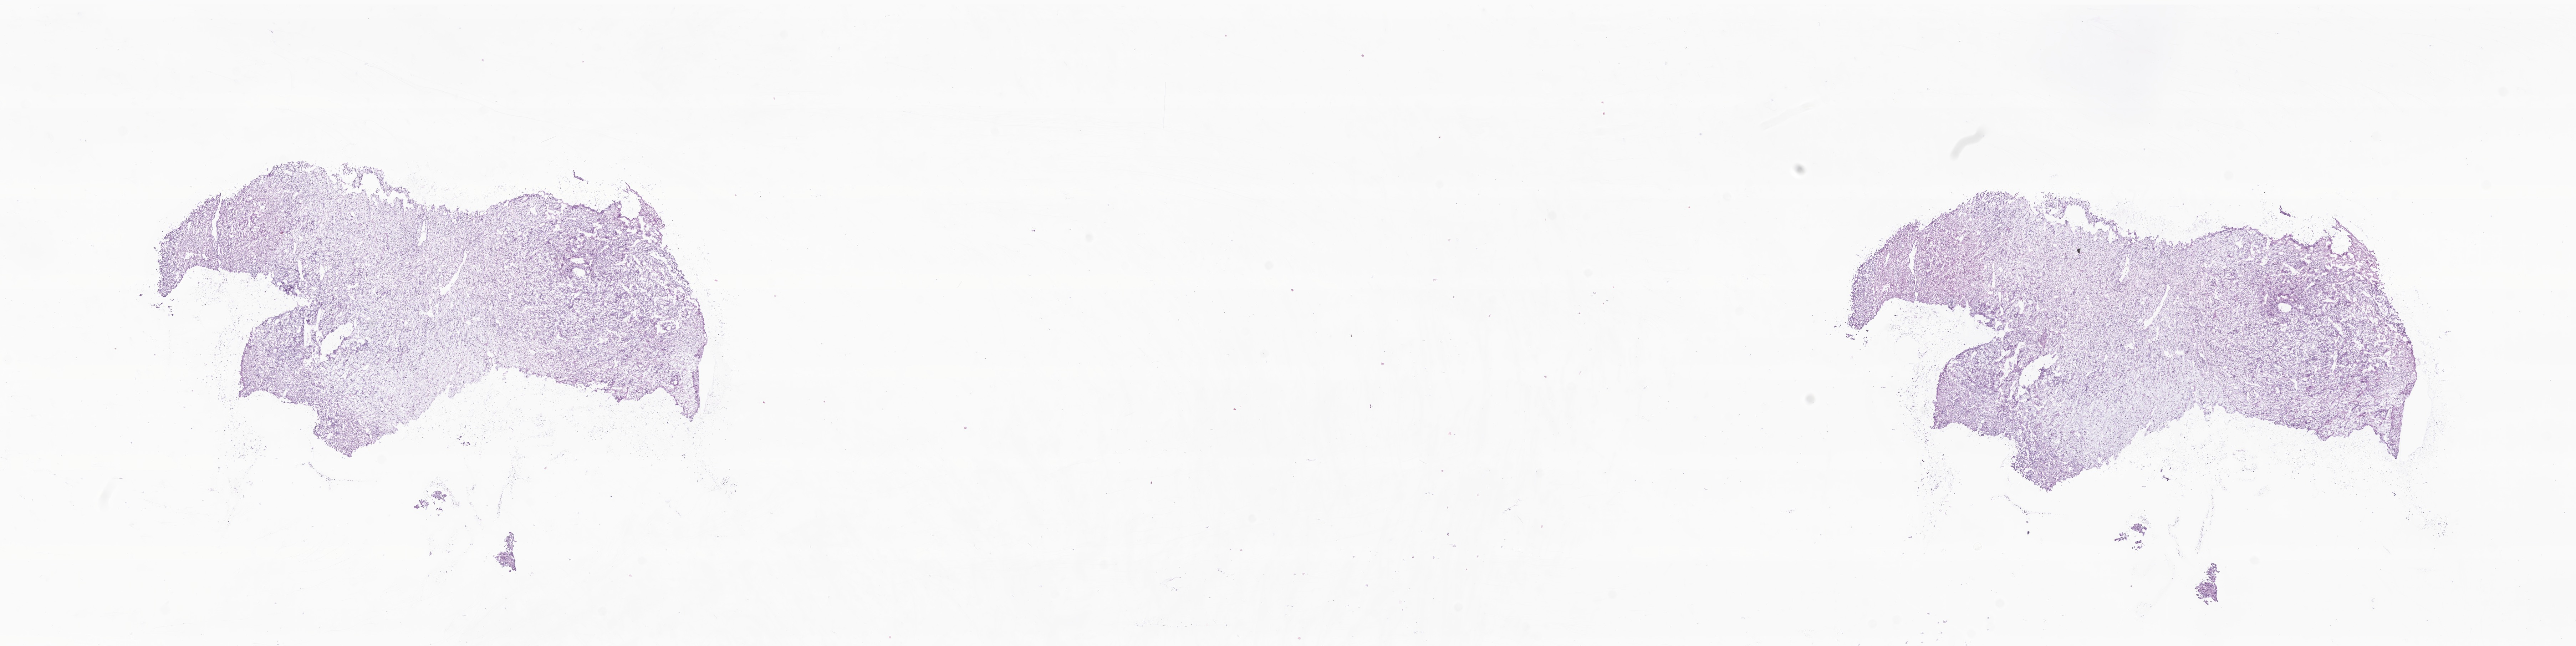
Digitized H&E-stained section of tumor tissue from the testis — a low-resolution overview of the entire scanned area, about 30.4 x 7.6 mm; frozen section. Male patient, age 194 months.
Recorded diagnosis: Rhabdomyosarcoma, NOS.